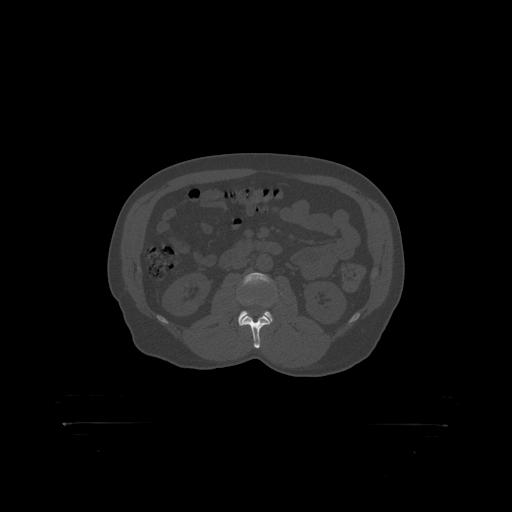
CT including the spine, one axial slice; slice 283 of 399 in the series (ordered by position); reconstruction kernel STANDARD; 120 kVp; bone window (W 1800 / L 400 HU); 1.25 mm slice thickness; 512 × 512 image matrix, field of view 650 × 650 mm. Male patient, age 46 years. Case-level facts recorded for this patient, not image findings: primary cancer: skin.
Structures marked on this image (semi-automatically segmented with operator editing):
- L2 vertebra: bounding box [x1, y1, x2, y2] px = [244, 316, 267, 319]
- L3 vertebra: [240, 273, 272, 318]